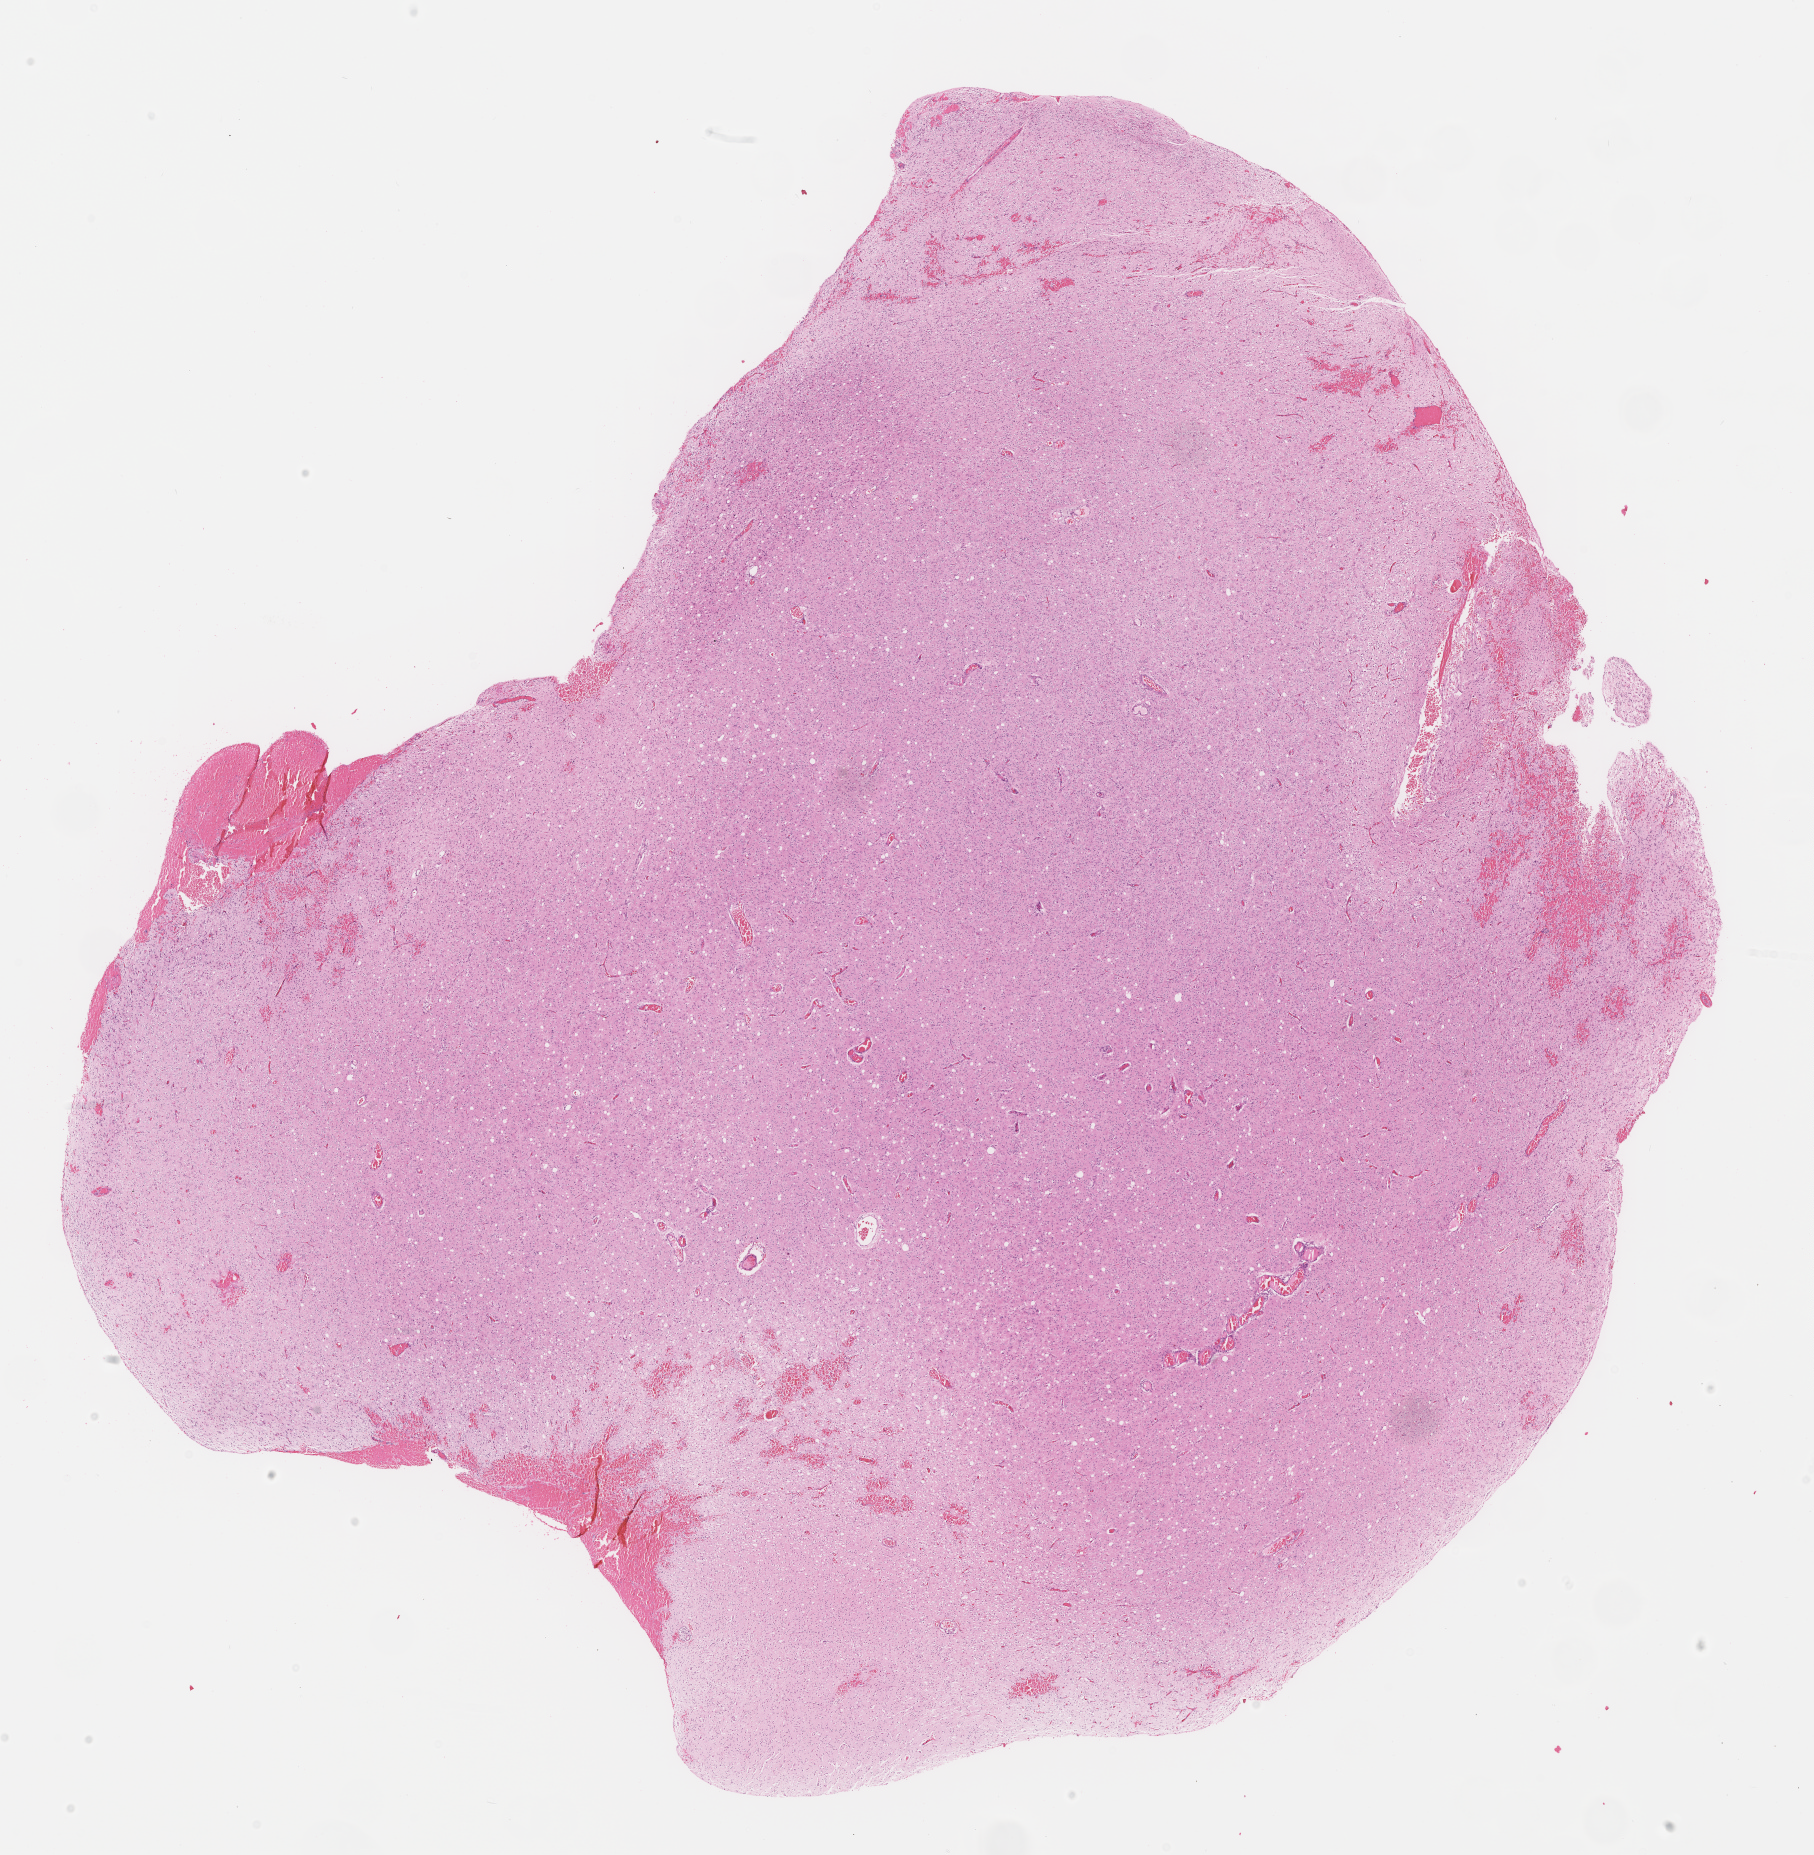
Whole-slide histology image, Hematoxylin and eosin (H&E) stained, shown as a low-resolution overview of the whole scanned area (about 14.6 x 14.9 mm, acquisition: 40x scan). Formalin-fixed paraffin-embedded (FFPE) diagnostic section. Sample: primary tumour, brain. Male patient; age at initial diagnosis 52 years.
Pathologic diagnosis: Oligodendroglioma, anaplastic (cerebrum).